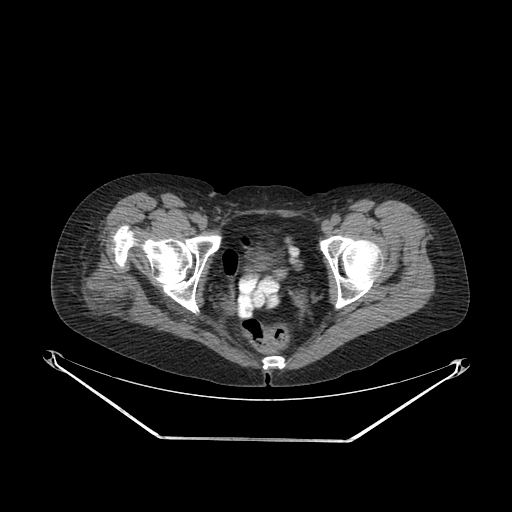
CT of an extremity soft-tissue mass (from a PET/CT study), one axial slice. Position 50 of 267 along the scan axis. Soft-tissue window (W 400 / L 40 HU). 512 × 512 image matrix. Female patient. From the clinical record (not read from this slice): histological type: epithelioid sarcoma with vascular differentiation; site of the primary tumour: right buttock.
Annotated regions visible in this slice (expert contour drawn on MRI and transferred to this co-registered scan by the dataset authors):
- gross tumour volume (mass): bounding box [x1, y1, x2, y2] px = [69, 262, 152, 325]